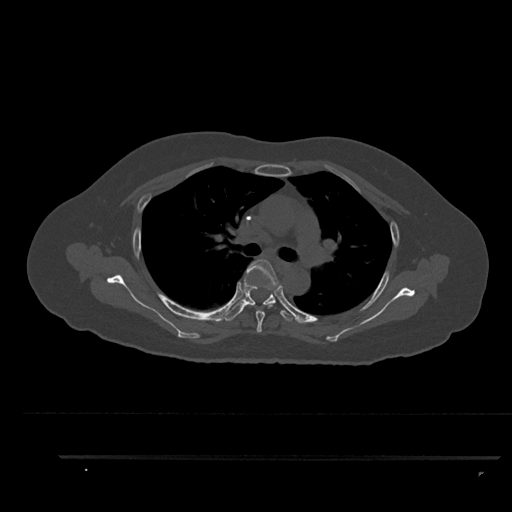
CT including the spine, one axial slice; position 621 of 797 along the scan axis; reconstruction kernel Br40s/3; 120 kVp; bone window (W 1800 / L 400 HU); 512 × 512 image matrix, field of view 408 × 408 mm. Patient: female, 44 years. From the clinical record (not read from this slice): primary cancer: renal.
Annotated regions visible in this slice (semi-automatic segmentation, software-assisted and operator-edited):
- T4 vertebra: bounding box [x1, y1, x2, y2] px = [246, 259, 281, 333]
- T5 vertebra: [225, 278, 295, 322]